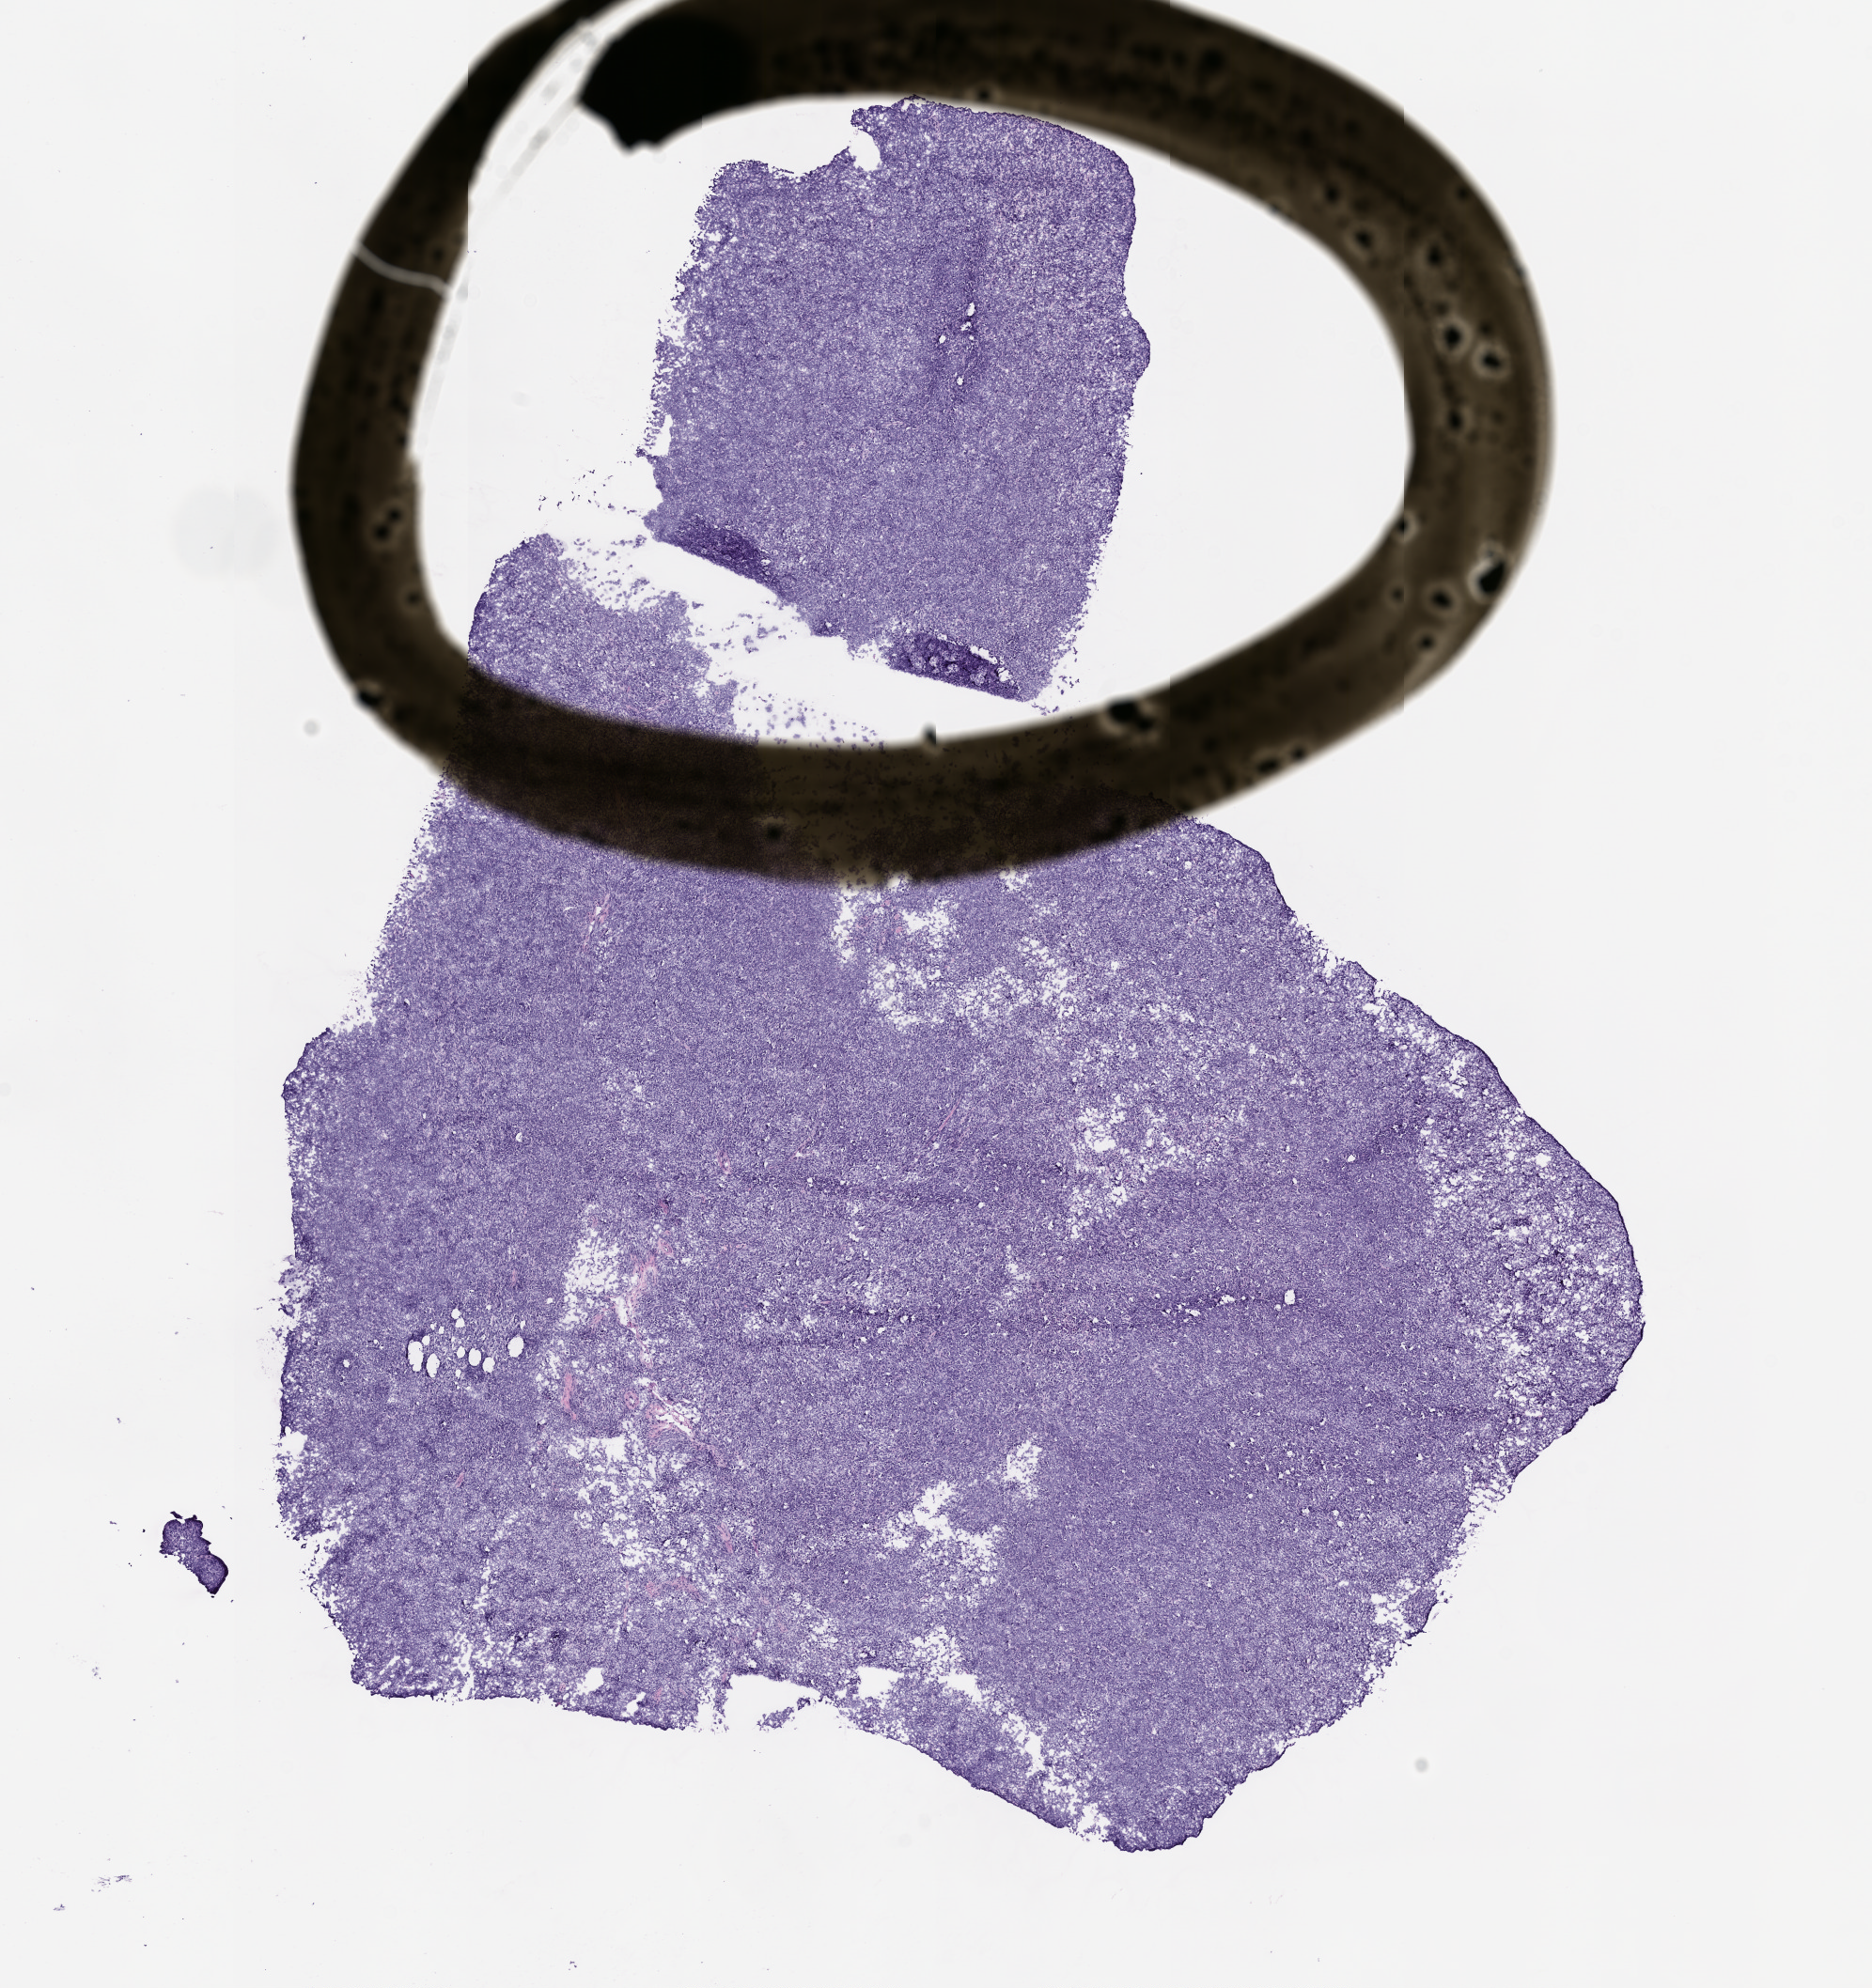
Haematoxylin and eosin whole-slide image of a patient-derived xenograft (PDX) tumor grown in a mouse, passage 2 — low-resolution overview of the scanned area, about 8.0 x 8.5 mm. Formalin-fixed paraffin-embedded section. Tumor site category: musculoskeletal.
Originating patient diagnosis: Synovial Sarcoma.